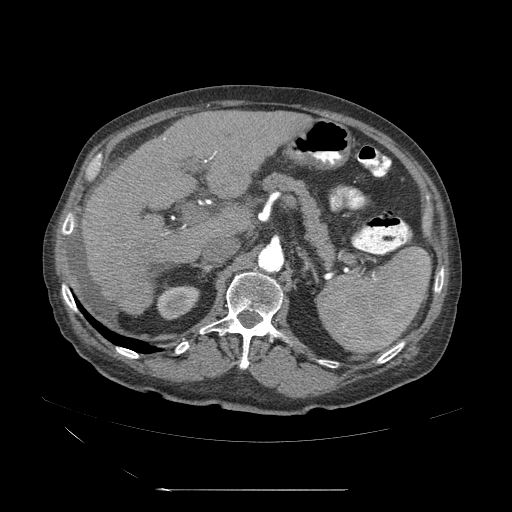
Contrast-enhanced abdominal CT (liver protocol), one axial slice. Slice 26 of 71 in the series (ordered by position). 120 kVp. Soft-tissue window (W 400 / L 40 HU). 2.5 mm slice thickness. 512 × 512 image matrix, field of view 440 × 440 mm. Case-level facts recorded for this patient, not image findings: diagnosis: hepatocellular carcinoma (patient treated with transarterial chemoembolisation; whether this scan precedes or follows treatment is not stated here); TNM stage (as recorded): Stage-II; Child-Pugh class: A; tumour nodularity: multinodular; tumour size: 1 cm.
Structures marked on this image (semi-automatically segmented with operator editing):
- abdominal aorta: bounding box [x1, y1, x2, y2] px = [258, 244, 285, 273]
- liver parenchyma outside the tumour (the mass and vessels are separate outlines, so this box may not span the whole liver): [79, 113, 294, 319]
- liver vessels: [145, 160, 239, 264]